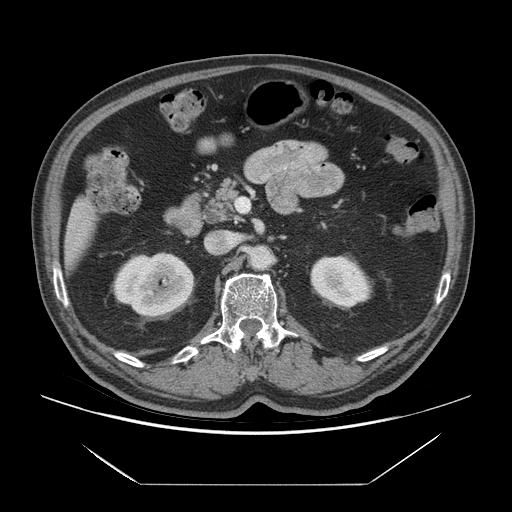
Contrast-enhanced abdominal CT (liver protocol), one axial slice; slice 25 of 75 in the series (ordered by position); 140 kVp; soft-tissue window (W 400 / L 40 HU); 512 × 512 image matrix. From the clinical record (not read from this slice): diagnosis: hepatocellular carcinoma (patient treated with transarterial chemoembolisation; whether this scan precedes or follows treatment is not stated here); TNM stage (as recorded): Stage-I; Child-Pugh class: A; tumour differentiation: well differentiated; tumour nodularity: uninodular.
Annotated regions visible in this slice (semi-automatic segmentation, software-assisted and operator-edited):
- liver parenchyma outside the tumour (the mass and vessels are separate outlines, so this box may not span the whole liver): bounding box <64,198,92,268> (left, top, right, bottom; pixels)